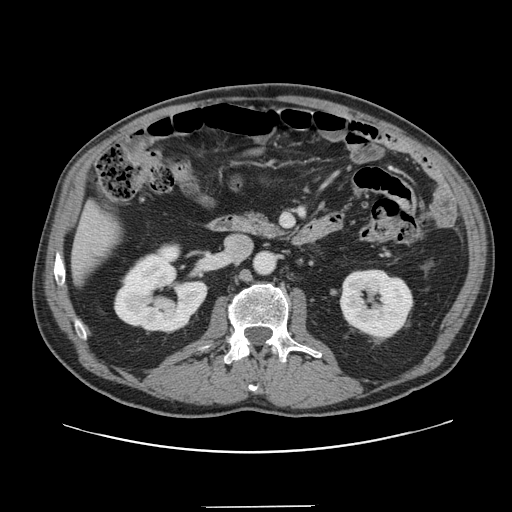
Contrast-enhanced abdominal CT, one axial slice. Position 55 of 139 along the scan axis. 120 kVp. Intravenous contrast given. Soft-tissue window (W 400 / L 40 HU). 512 × 512 image matrix. Male patient, age 64 years. From the clinical record (not read from this slice): diagnosis: colorectal cancer liver metastases, imaged before liver resection; multiple liver metastases: yes; largest metastasis: 3.5 cm; disease in both lobes: yes.
Outlined on this slice (expert manual segmentation):
- liver: bounding box (x1, y1, x2, y2) in pixels: (74, 207, 118, 280)
- planned liver remnant (the part of the liver to remain after resection): (73, 208, 118, 279)